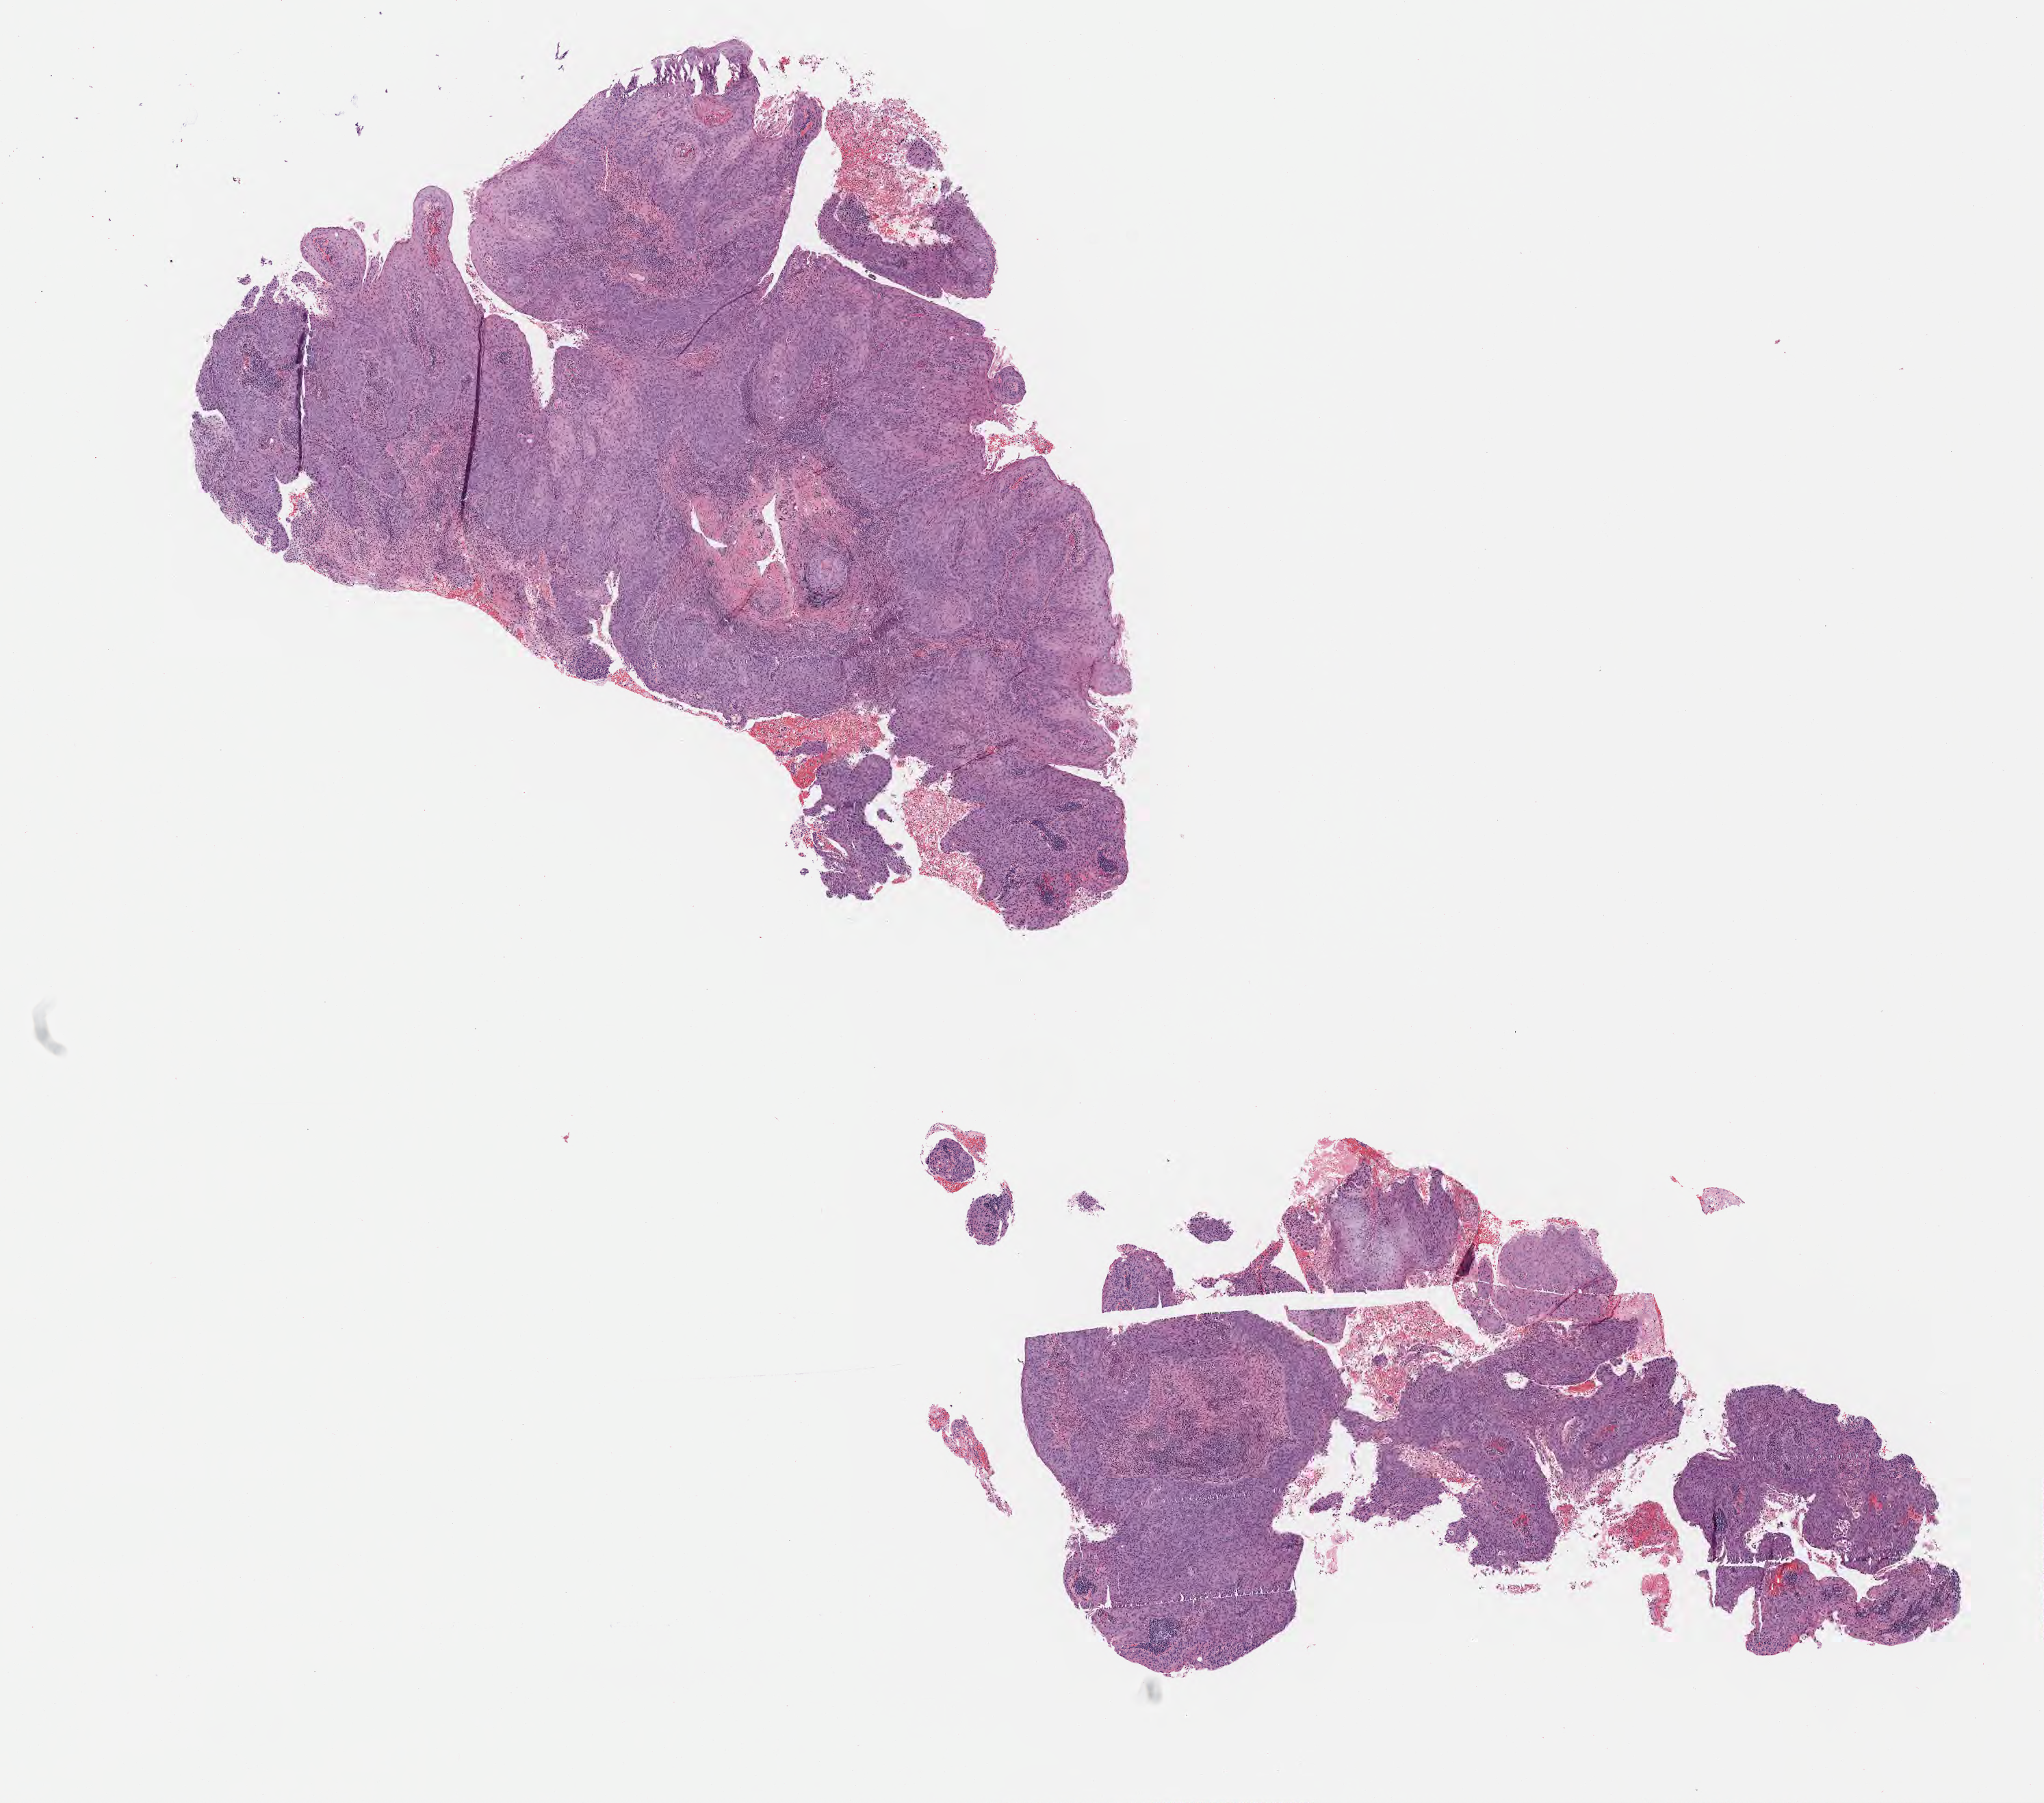
Hematoxylin and eosin (H&E) whole-slide image — a low-resolution overview of the entire scanned area, about 12.1 x 10.7 mm. Tumor tissue. Site: cervix. Patient female; aged 29.
• diagnosis: Squamous cell carcinoma, keratinizing, NOS